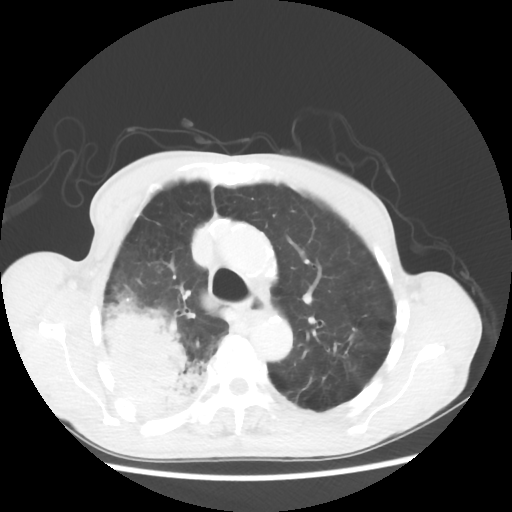
Chest CT, one axial slice. Slice 39 of 58 in the series (ordered by position). 100 kVp. Lung window (W 1500 / L -600 HU). 5 mm slice thickness. 512 × 512 image matrix. Patient: male, 75 years. Case-level facts recorded for this patient, not image findings: clinical TNM (as recorded): T4 N1 M1.
Structures marked on this image (bounding box drawn by a radiologist):
- lung tumour (recorded histology: adenocarcinoma): bounding box [x1, y1, x2, y2] px = [98, 288, 212, 420]